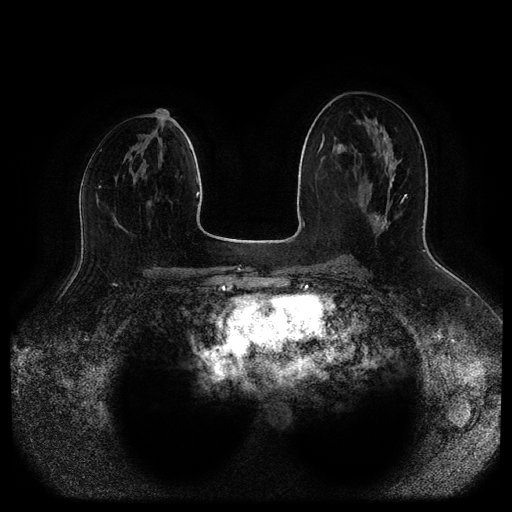
Breast MRI (dynamic contrast-enhanced, multi-phase), one axial slice. Position 49 of 116 along the scan axis. Dynamic contrast-enhanced series, time point 2 of 5 at this slice position (early post-contrast). 1.5 T. TE 2.6 ms, TR 5.2 ms. 2 mm slice thickness. 512 × 512 image matrix, field of view 380 × 380 mm. Patient: female, 45 years.
Annotated regions visible in this slice (semi-automatically segmented with operator editing):
- breast lesion (labelled benign in the annotation): bounding box (x1, y1, x2, y2) in pixels: (368, 214, 387, 234)